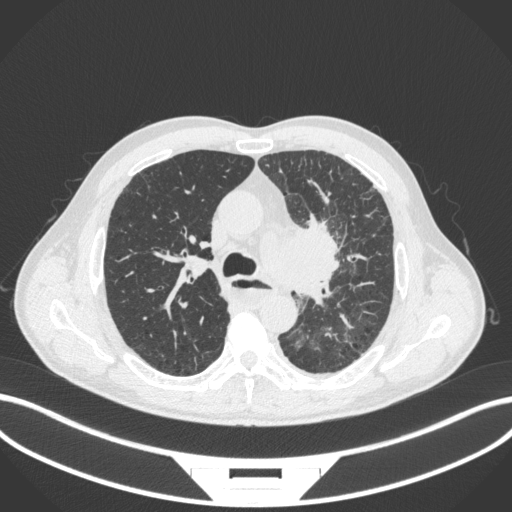
Chest CT, one axial slice; position 256 of 411 along the scan axis; reconstruction kernel B31f; 120 kVp; lung window (W 1500 / L -600 HU); 1 mm slice thickness; 512 × 512 image matrix, field of view 400 × 400 mm. Male patient, age 57 years. From the clinical record (not read from this slice): clinical TNM (as recorded): T2a N1 M0.
Outlined on this slice (rectangle marked by the reading radiologist):
- lung tumour (recorded histology: squamous cell carcinoma): bounding box (x1, y1, x2, y2) in pixels: (259, 209, 350, 303)